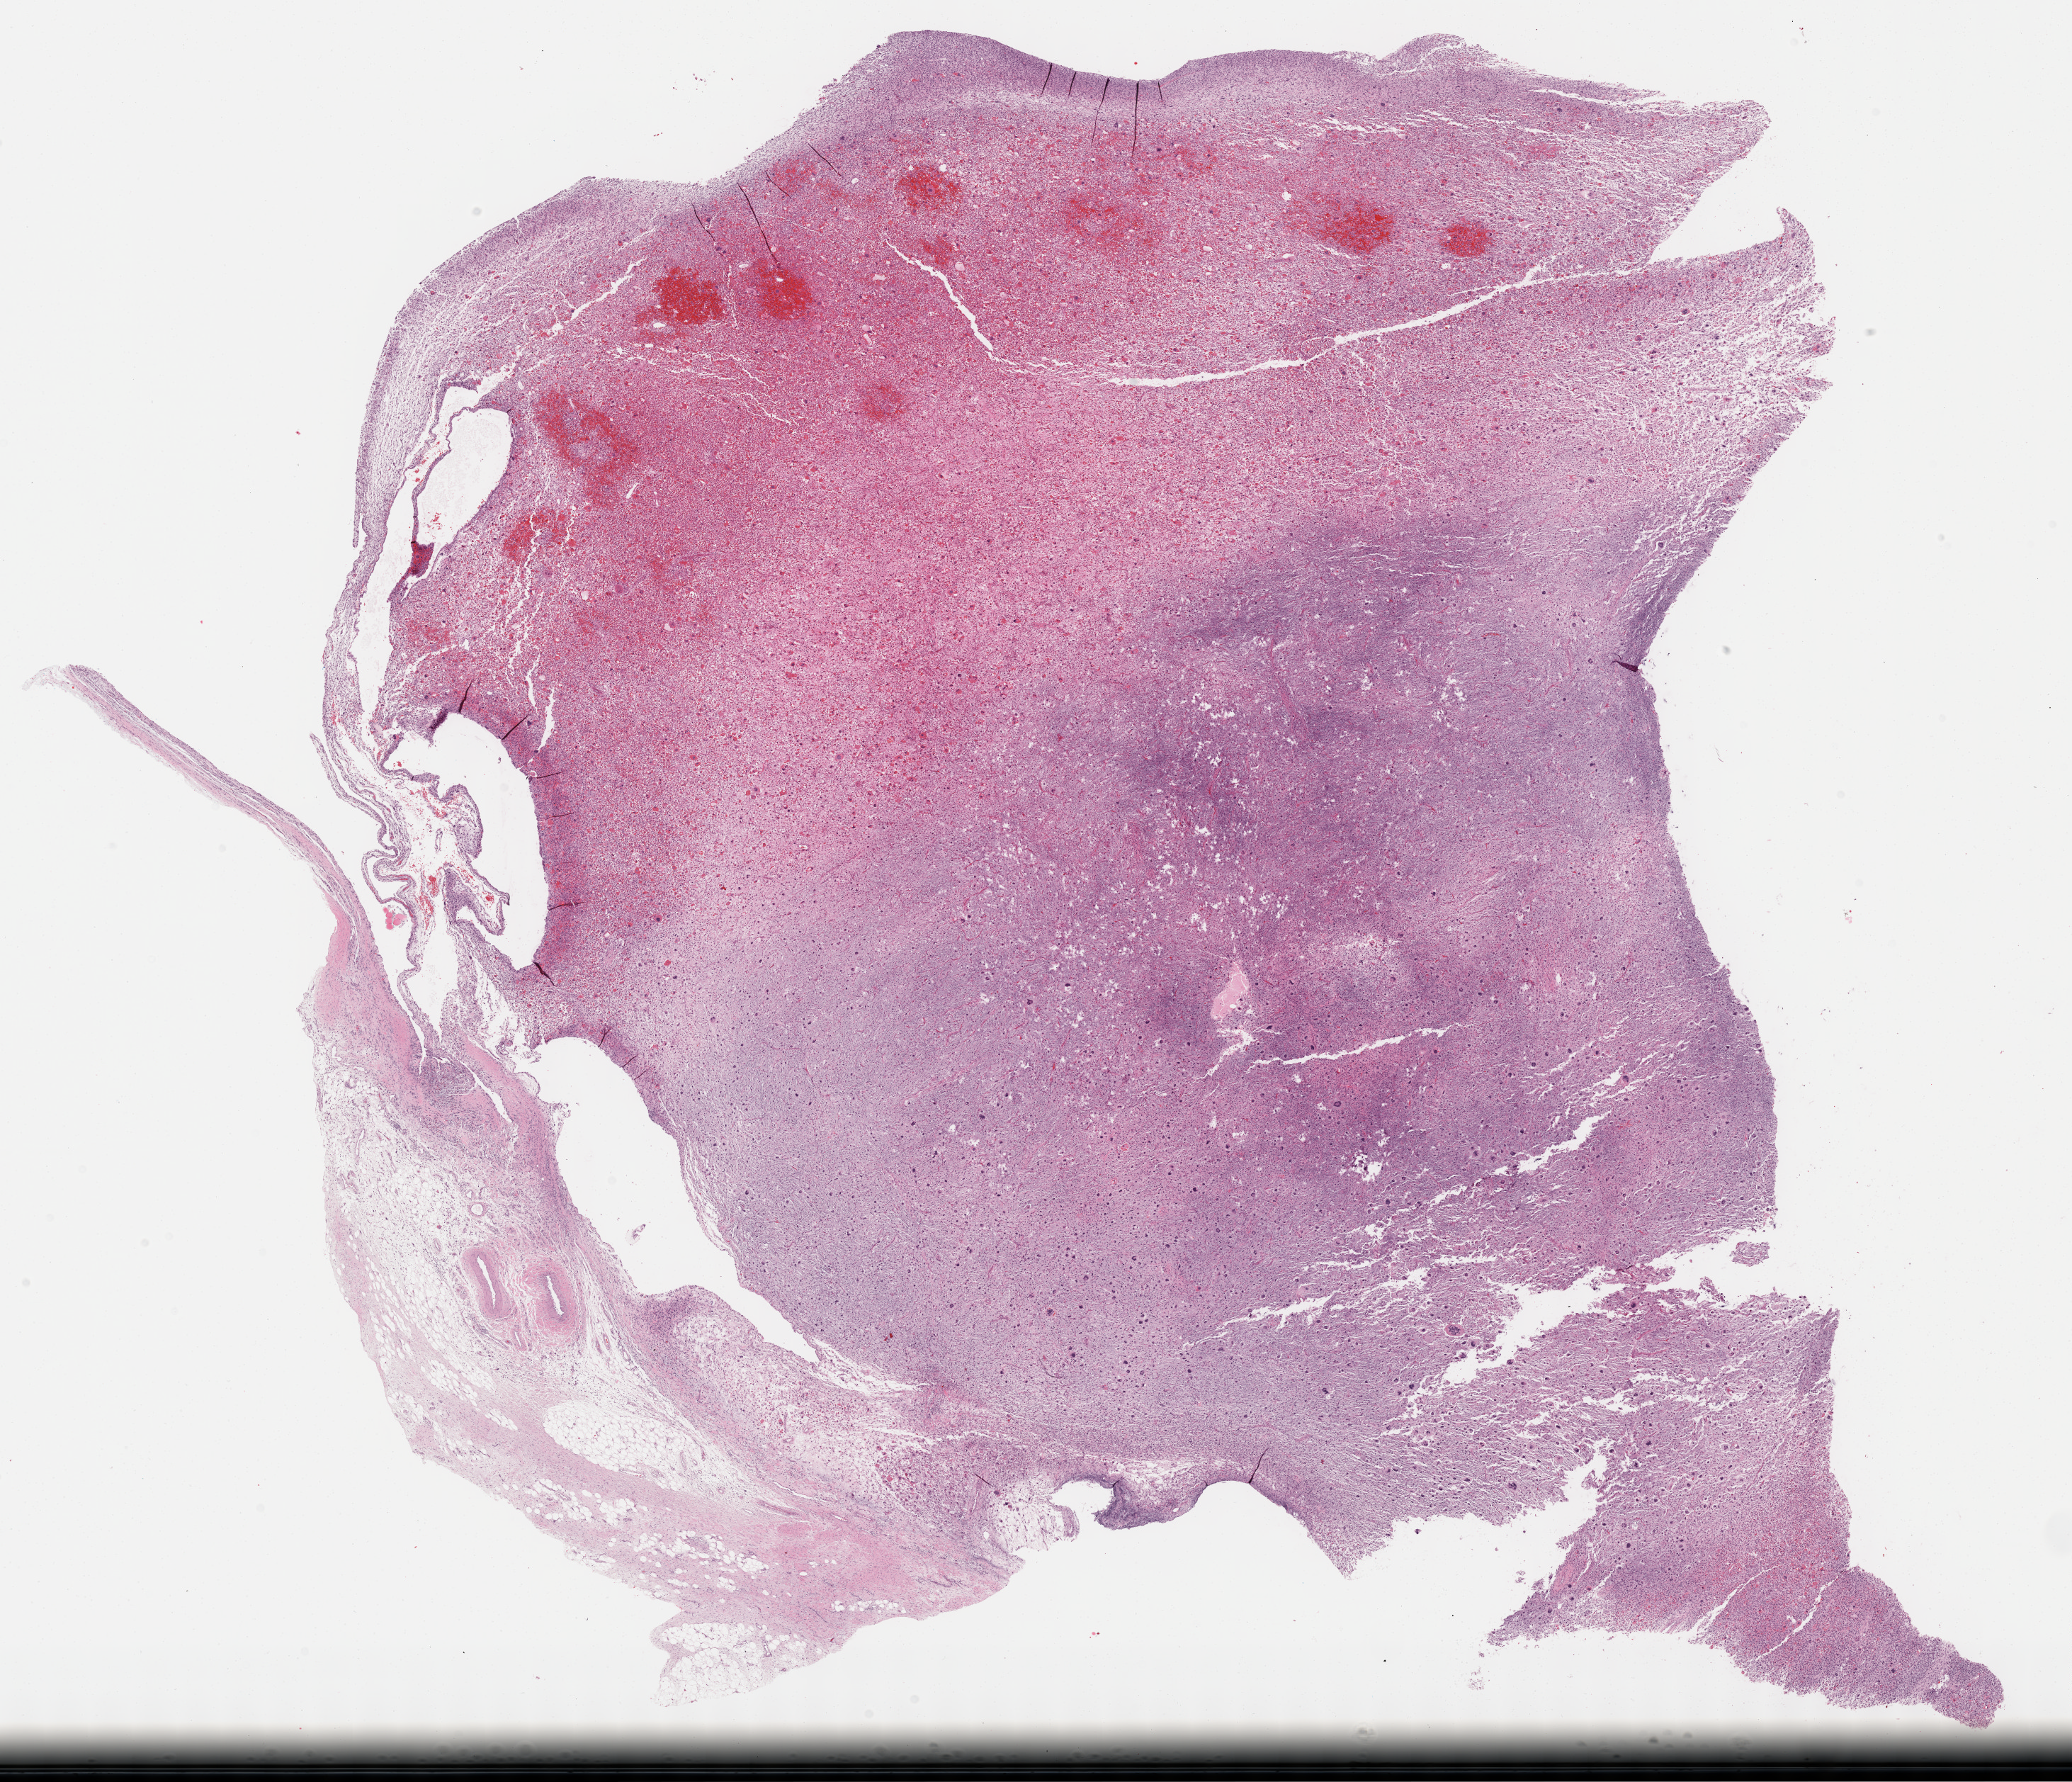
Whole-slide histology image, H&E, a low-resolution overview of the entire scanned area, about 23.7 x 20.3 mm, formalin-fixed paraffin-embedded (FFPE) diagnostic section, sample: primary tumour, connective, subcutaneous and other soft tissues. Patient: female, age at initial diagnosis 54 years.
Histologic diagnosis: Fibromyxosarcoma (connective, subcutaneous and other soft tissues of lower limb and hip).